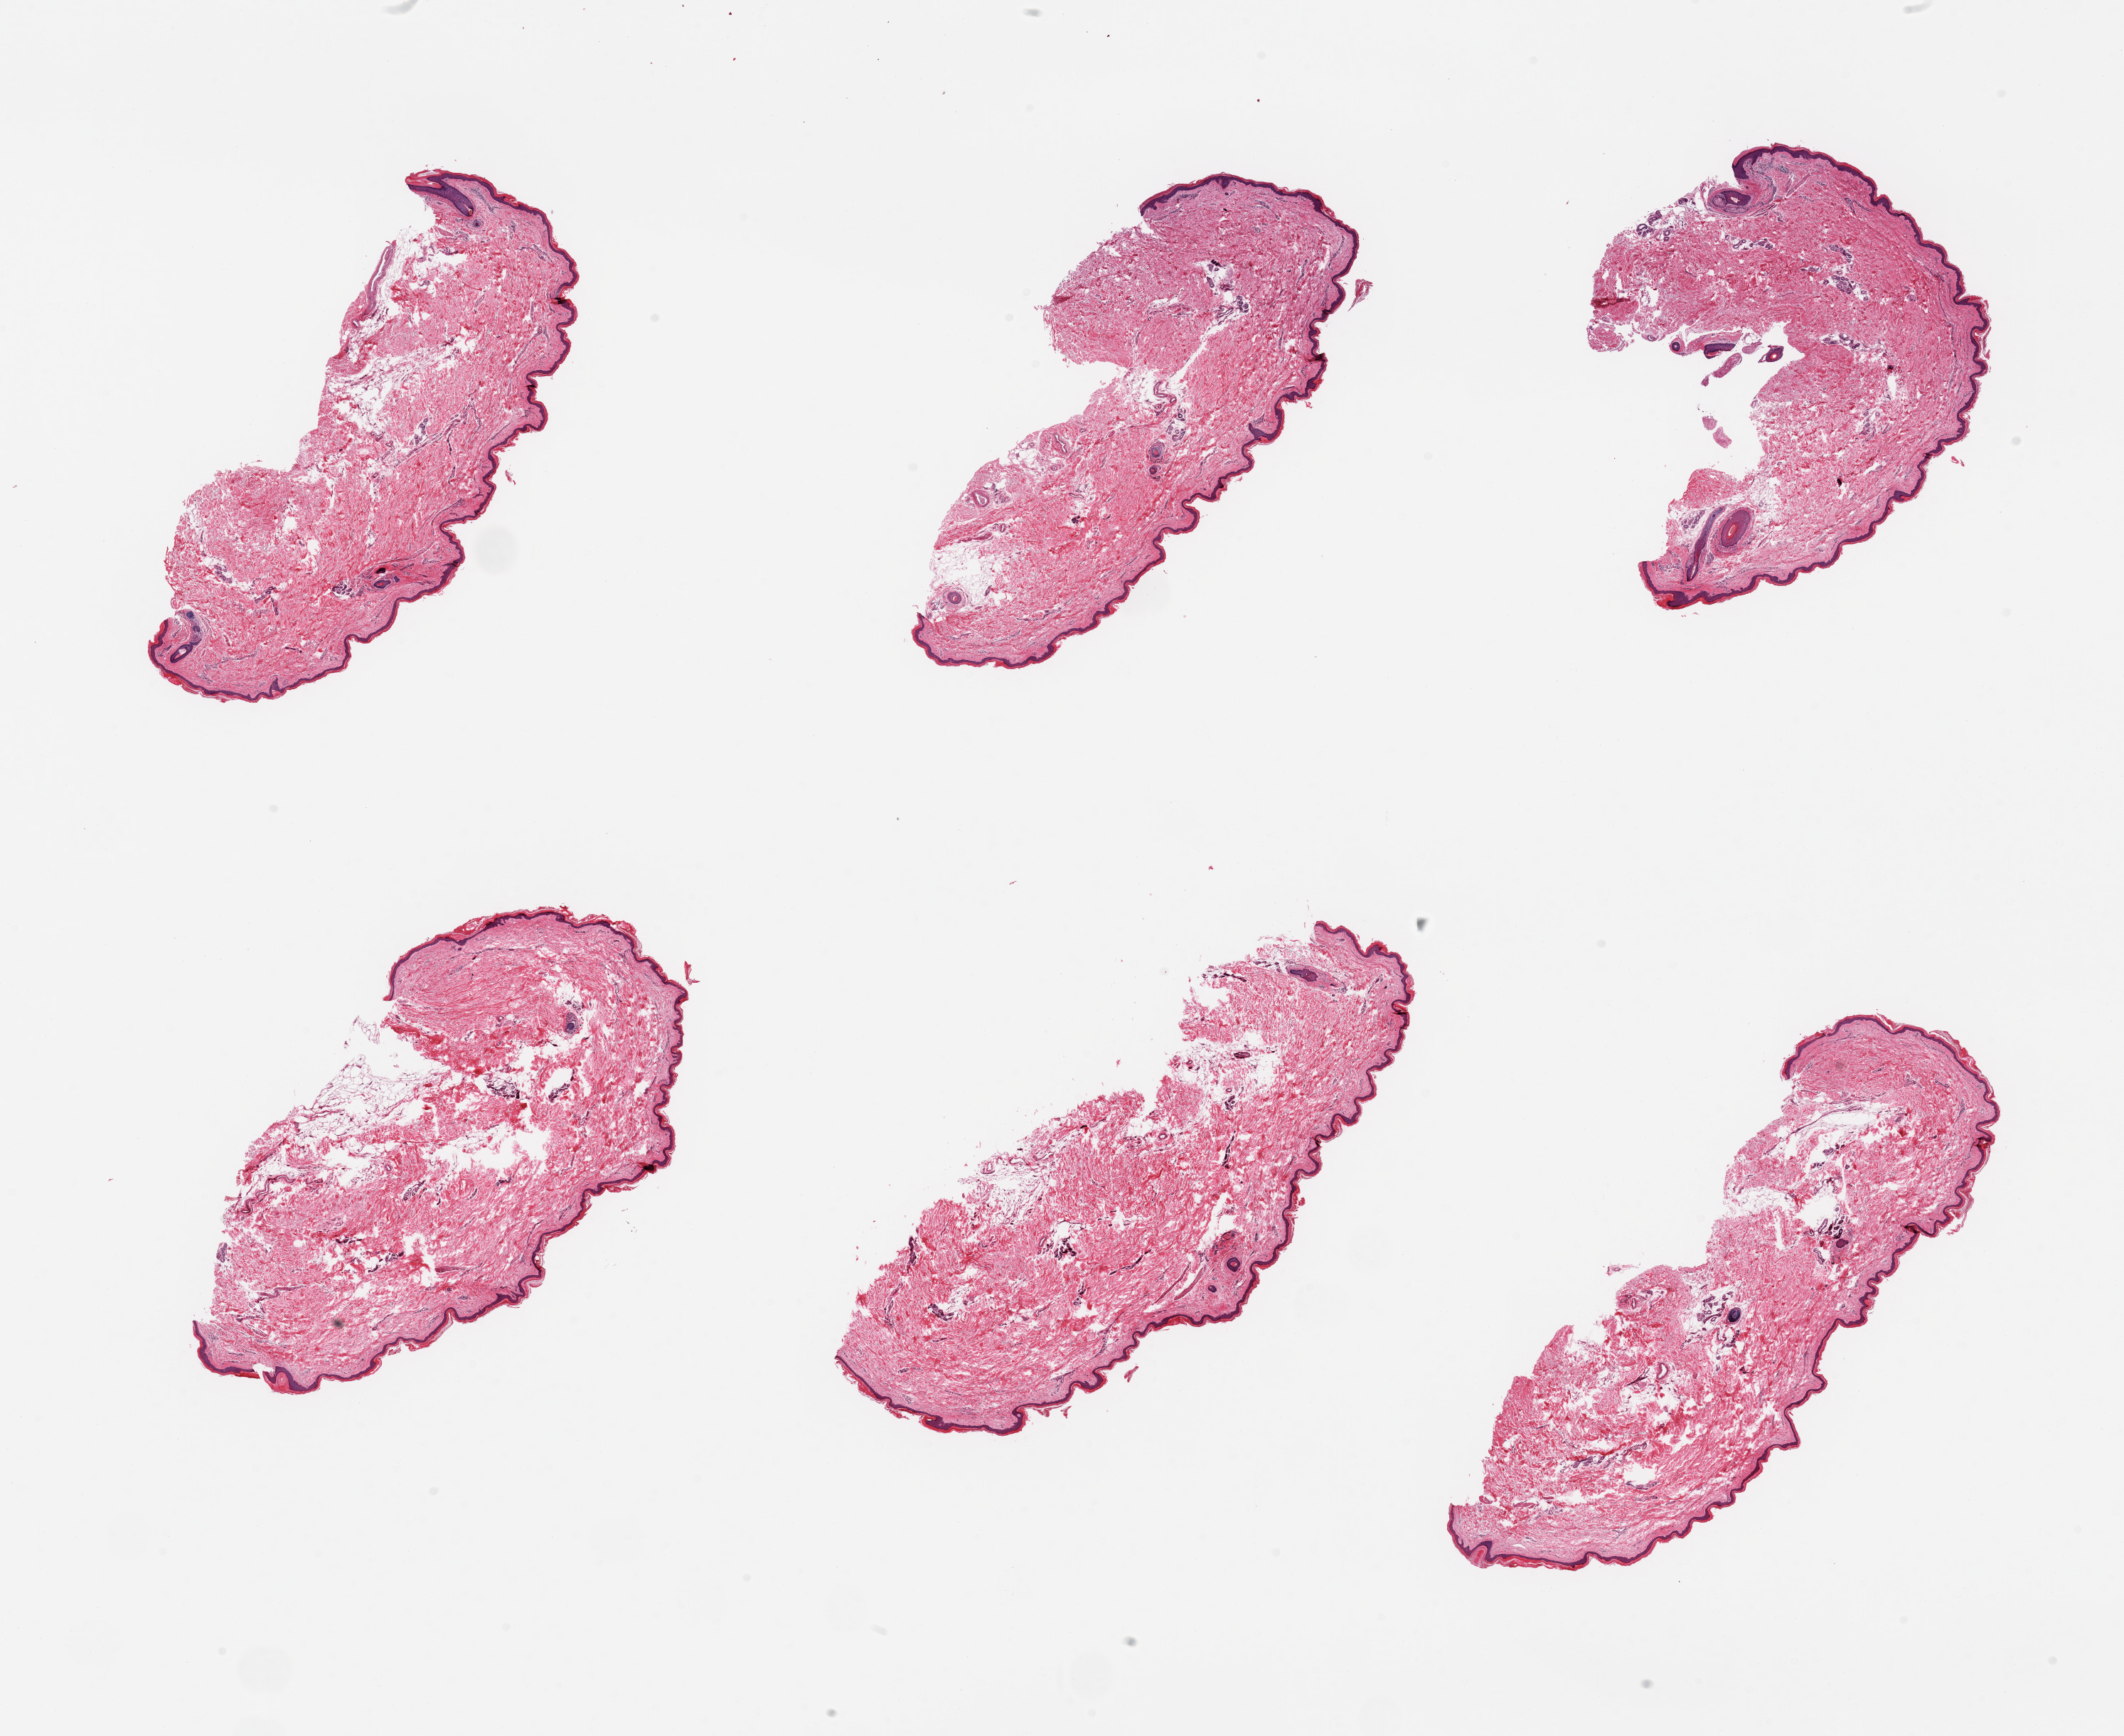
Whole-slide image, H&E stain — whole scanned area (about 23.6 x 19.3 mm) shown as a low-resolution overview; PAXgene-fixed, paraffin-embedded tissue; sampled site (target tissue): skin of lower leg; donor tissue sample. Donor sex: male.
Pathologist's review note for this sample: 6 pieces; minimal dermal fat; squamous epithelium is ~50 microns.